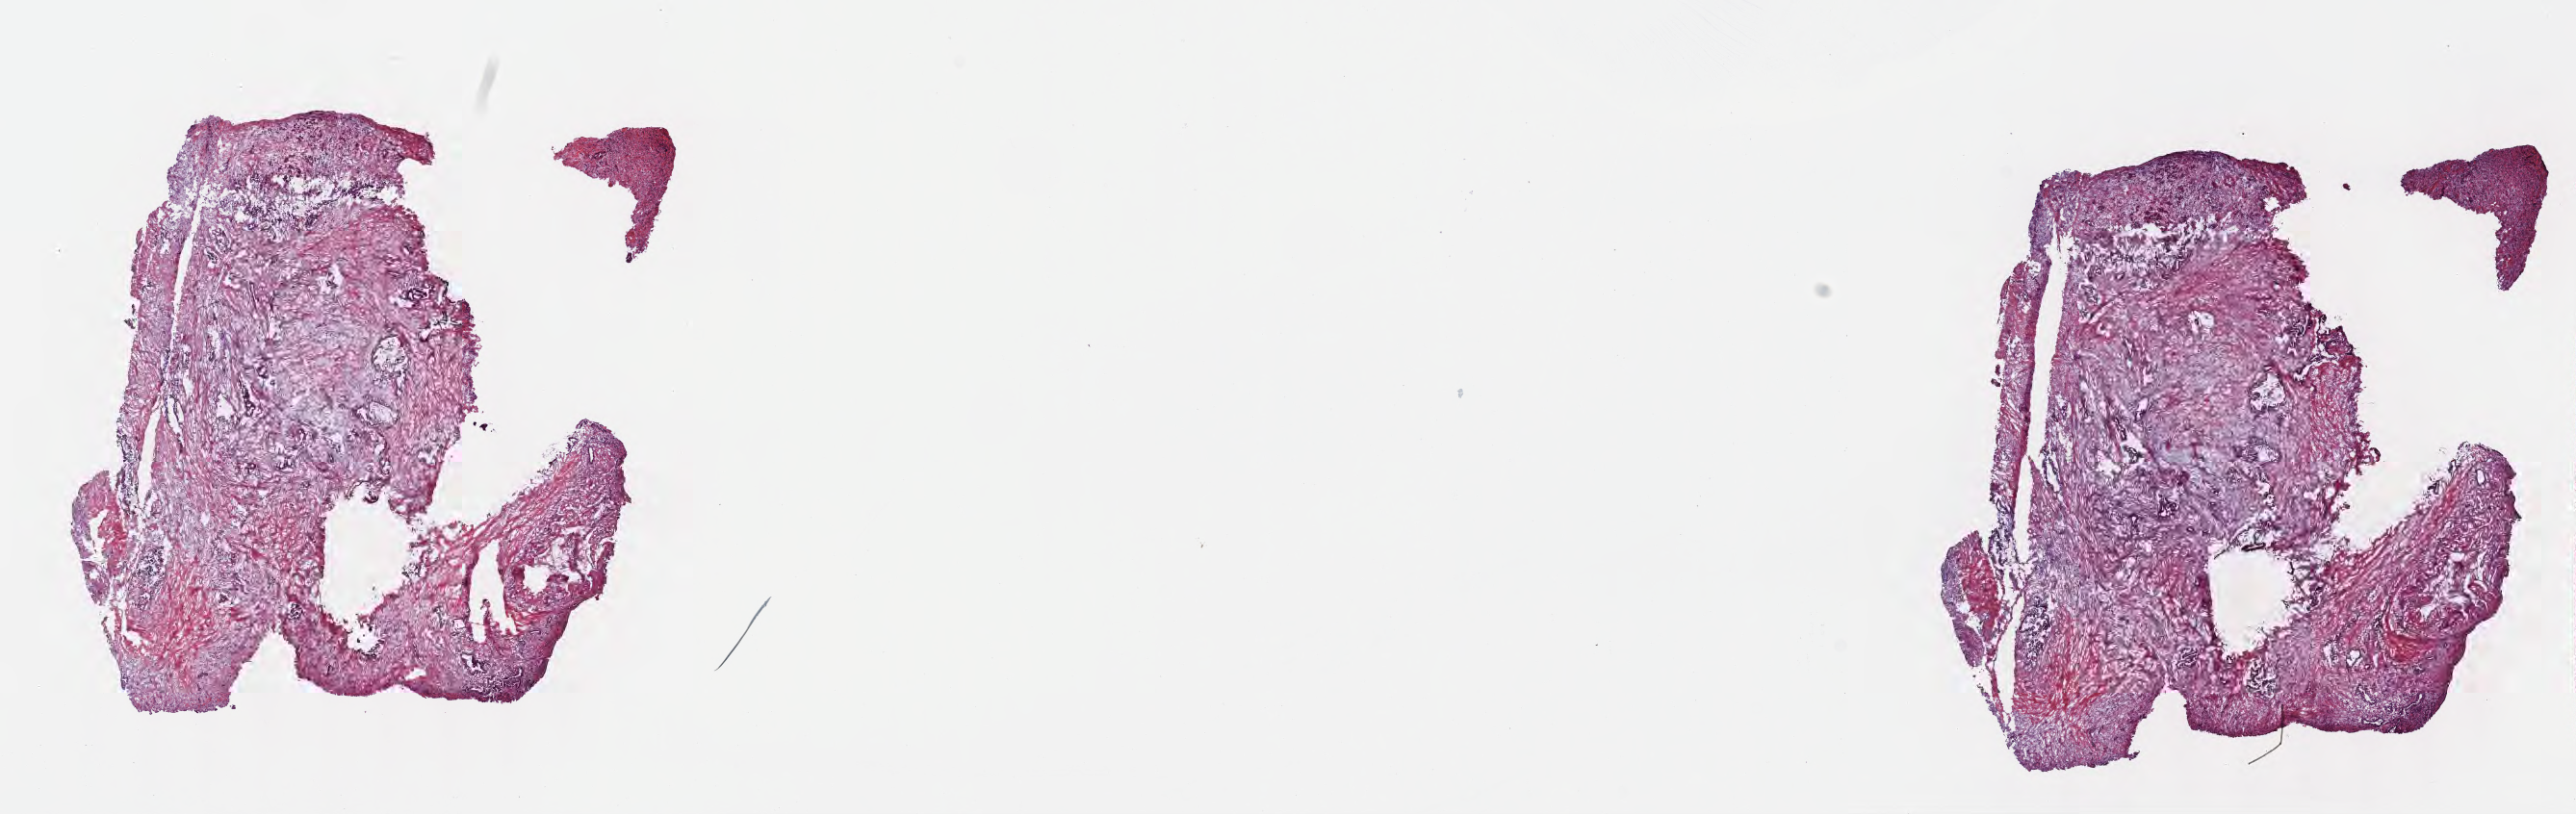
Digitized hematoxylin and eosin (H&E)-stained section, whole scanned area (about 21.6 x 6.8 mm) shown as a low-resolution overview; frozen section; primary tumor; site: head of pancreas. Female, age 74 years at initial diagnosis. Tumor grade: G2 (moderately differentiated). Slide review estimates, as recorded: tumor cells 25%, tumor nuclei 25%, stromal cells 70%, necrosis 0%, normal cells 5%. Infiltration values recorded for this section: lymphocyte infiltration 5%, monocyte infiltration 0%, neutrophil infiltration 0%.
• section: top of the tissue portion
• AJCC pathologic stage: Stage III
• histologic diagnosis: Infiltrating duct carcinoma, NOS